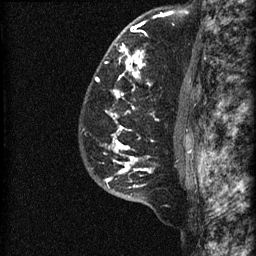
Breast MRI (dynamic contrast-enhanced), one sagittal slice; slice 48 of 60 in the series (ordered by position); dynamic contrast-enhanced series, image 2 of 3 at this slice position (ordered by acquisition); 1.5 T; TE 4.2 ms, TR 22.7 ms; 1.5 mm slice thickness; 256 × 256 image matrix, field of view 180 × 180 mm. Female patient, age 48 years. Case-level facts recorded for this patient, not image findings: setting: breast cancer imaged before/during neoadjuvant chemotherapy; receptor status: triple-negative.
Annotated regions visible in this slice (semi-automatic segmentation, software-assisted and operator-edited):
- analysis volume of interest (the breast-tissue region the enhancement analysis was run in; not a lesion): bounding box (x1, y1, x2, y2) in pixels: (81, 23, 186, 202)
- tumour enhancement mask (voxels above the 90 % enhancement threshold inside the analysis volume of interest): (95, 25, 152, 187)